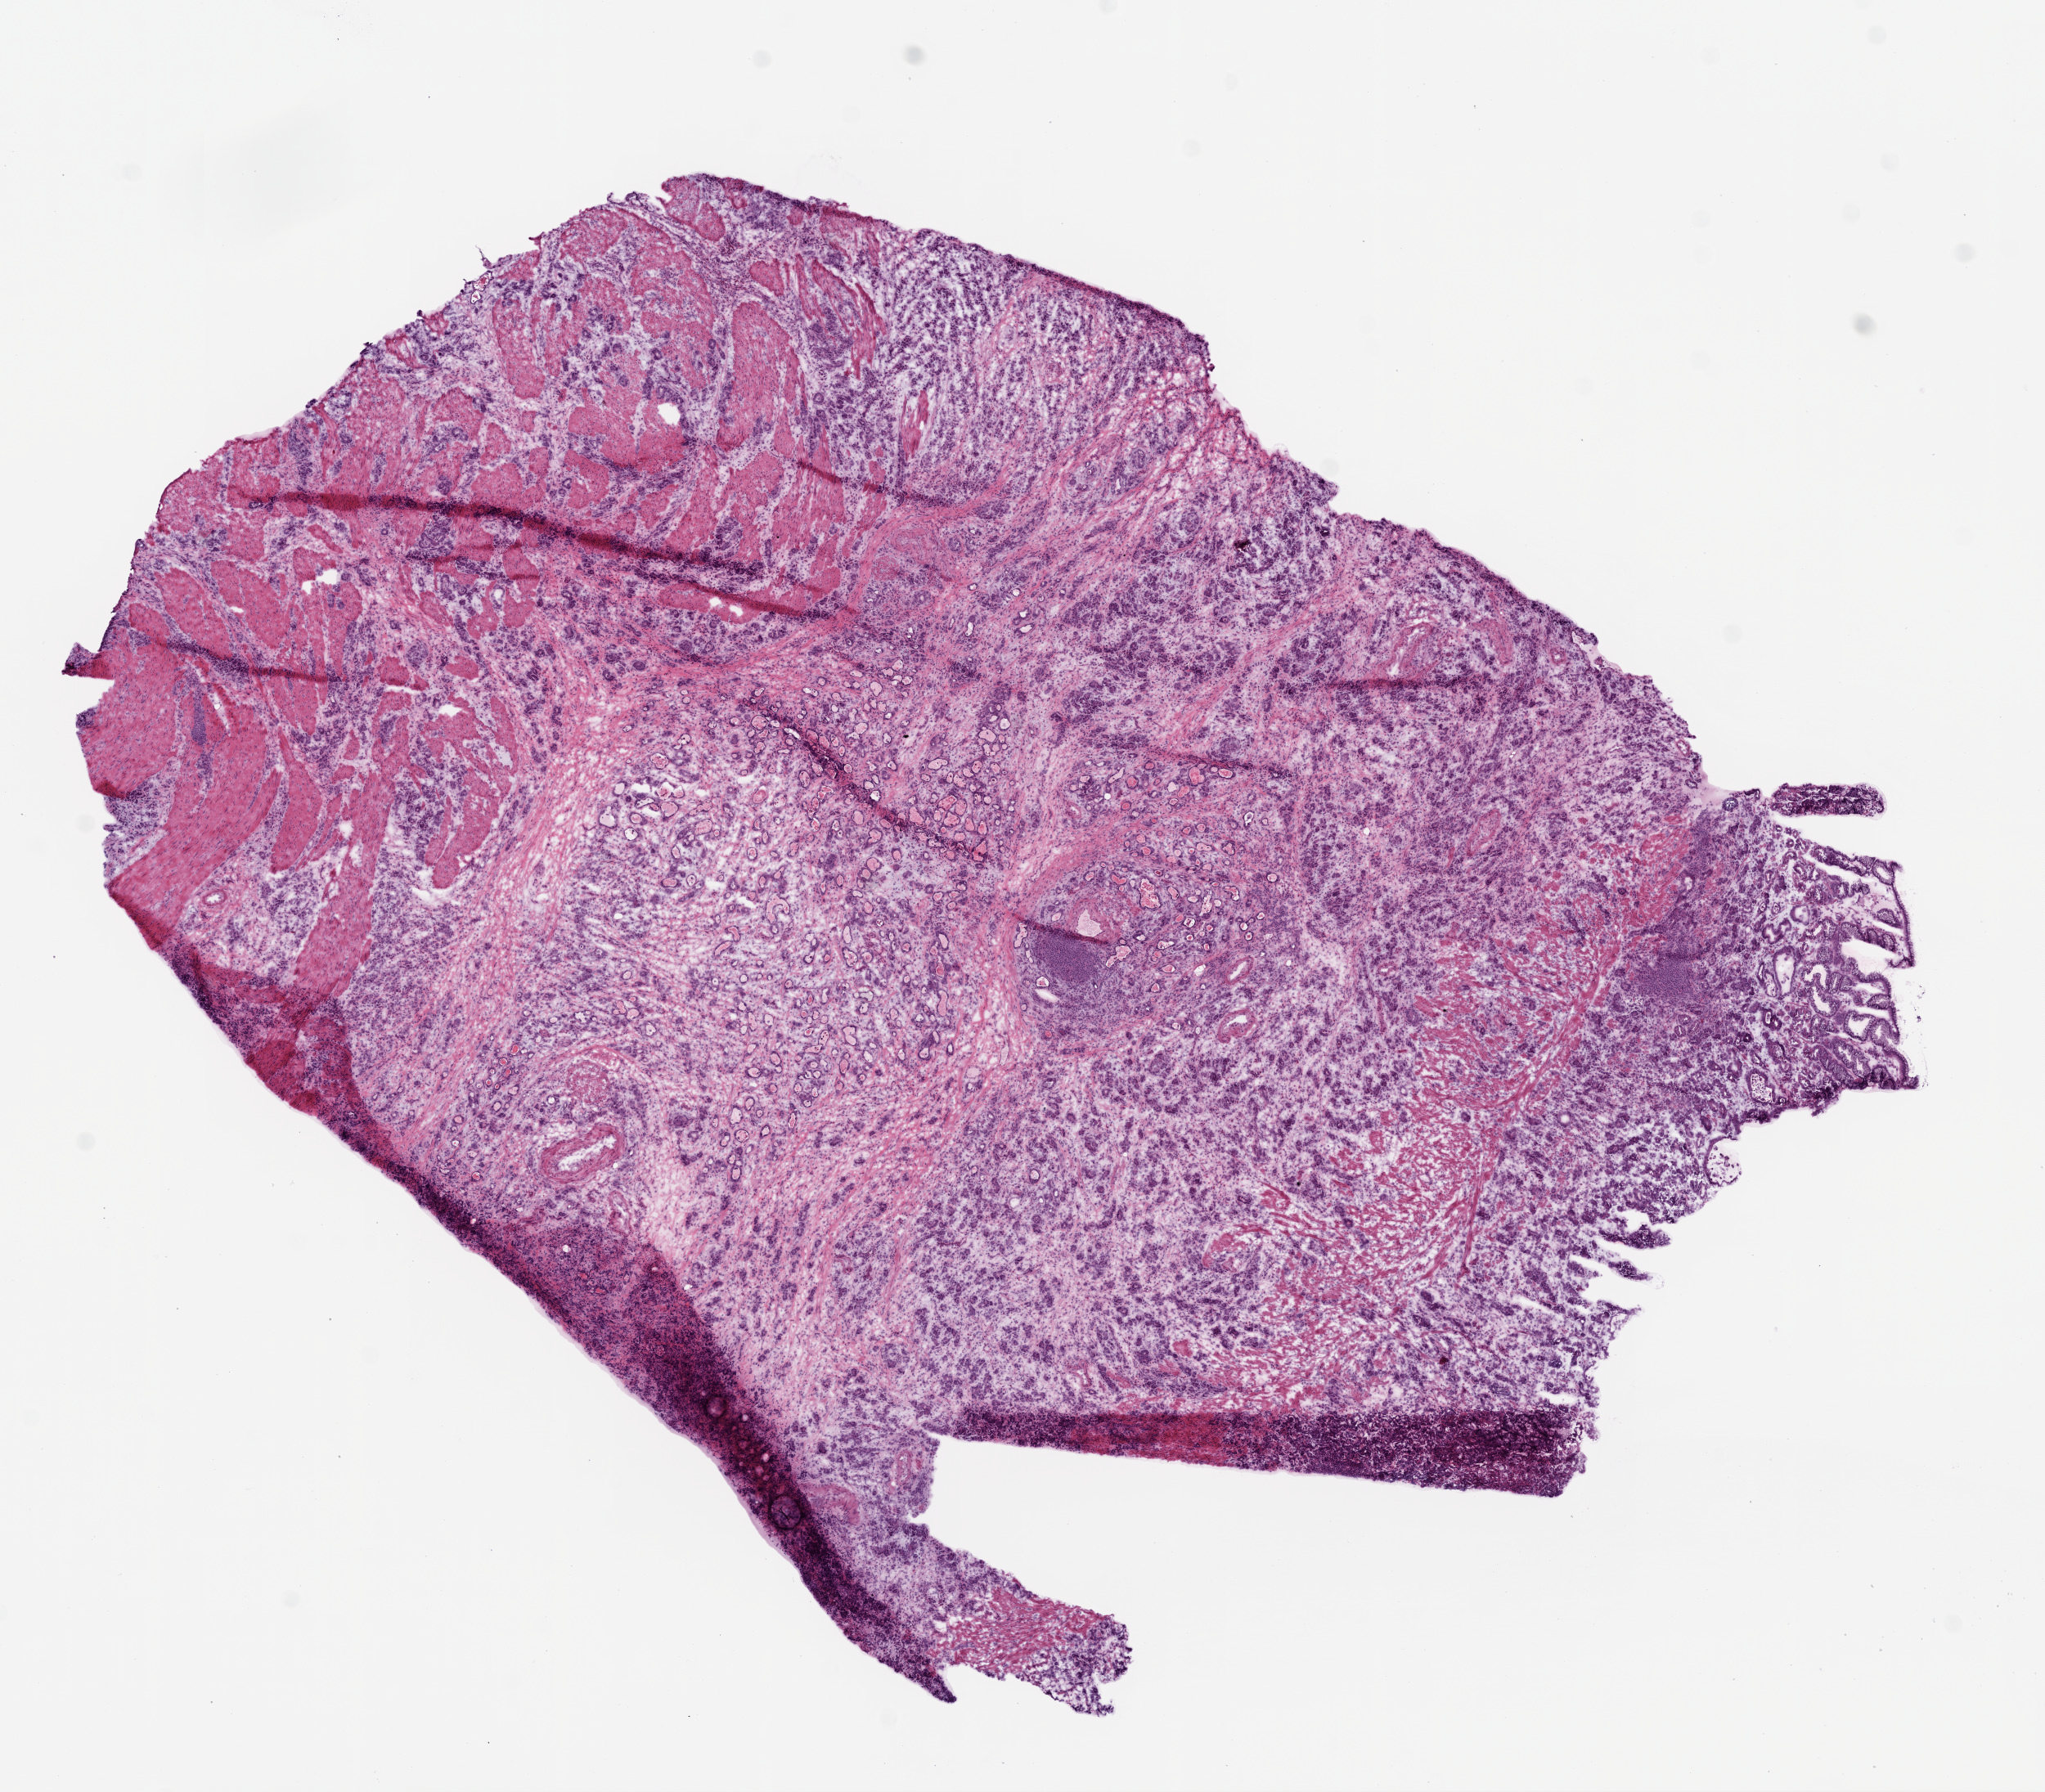
Digitized Hematoxylin and eosin (H&E) stained tissue section (whole slide), shown as a low-resolution overview of the whole scanned area (about 10.0 x 8.8 mm, from a 20x scan). Frozen section from the bottom of the tissue portion. Sample: primary tumour, stomach. Male patient; age at initial diagnosis 69 years. Histologic grade: G3 (poorly differentiated). Pathologist review of this section (percent, as recorded): tumour cells 70%, tumour nuclei 75%, normal cells 5%, stromal cells 20%, necrosis 5%.
Diagnosis: Carcinoma, diffuse type (body of stomach). AJCC pathologic stage: IIIC (7th edition).